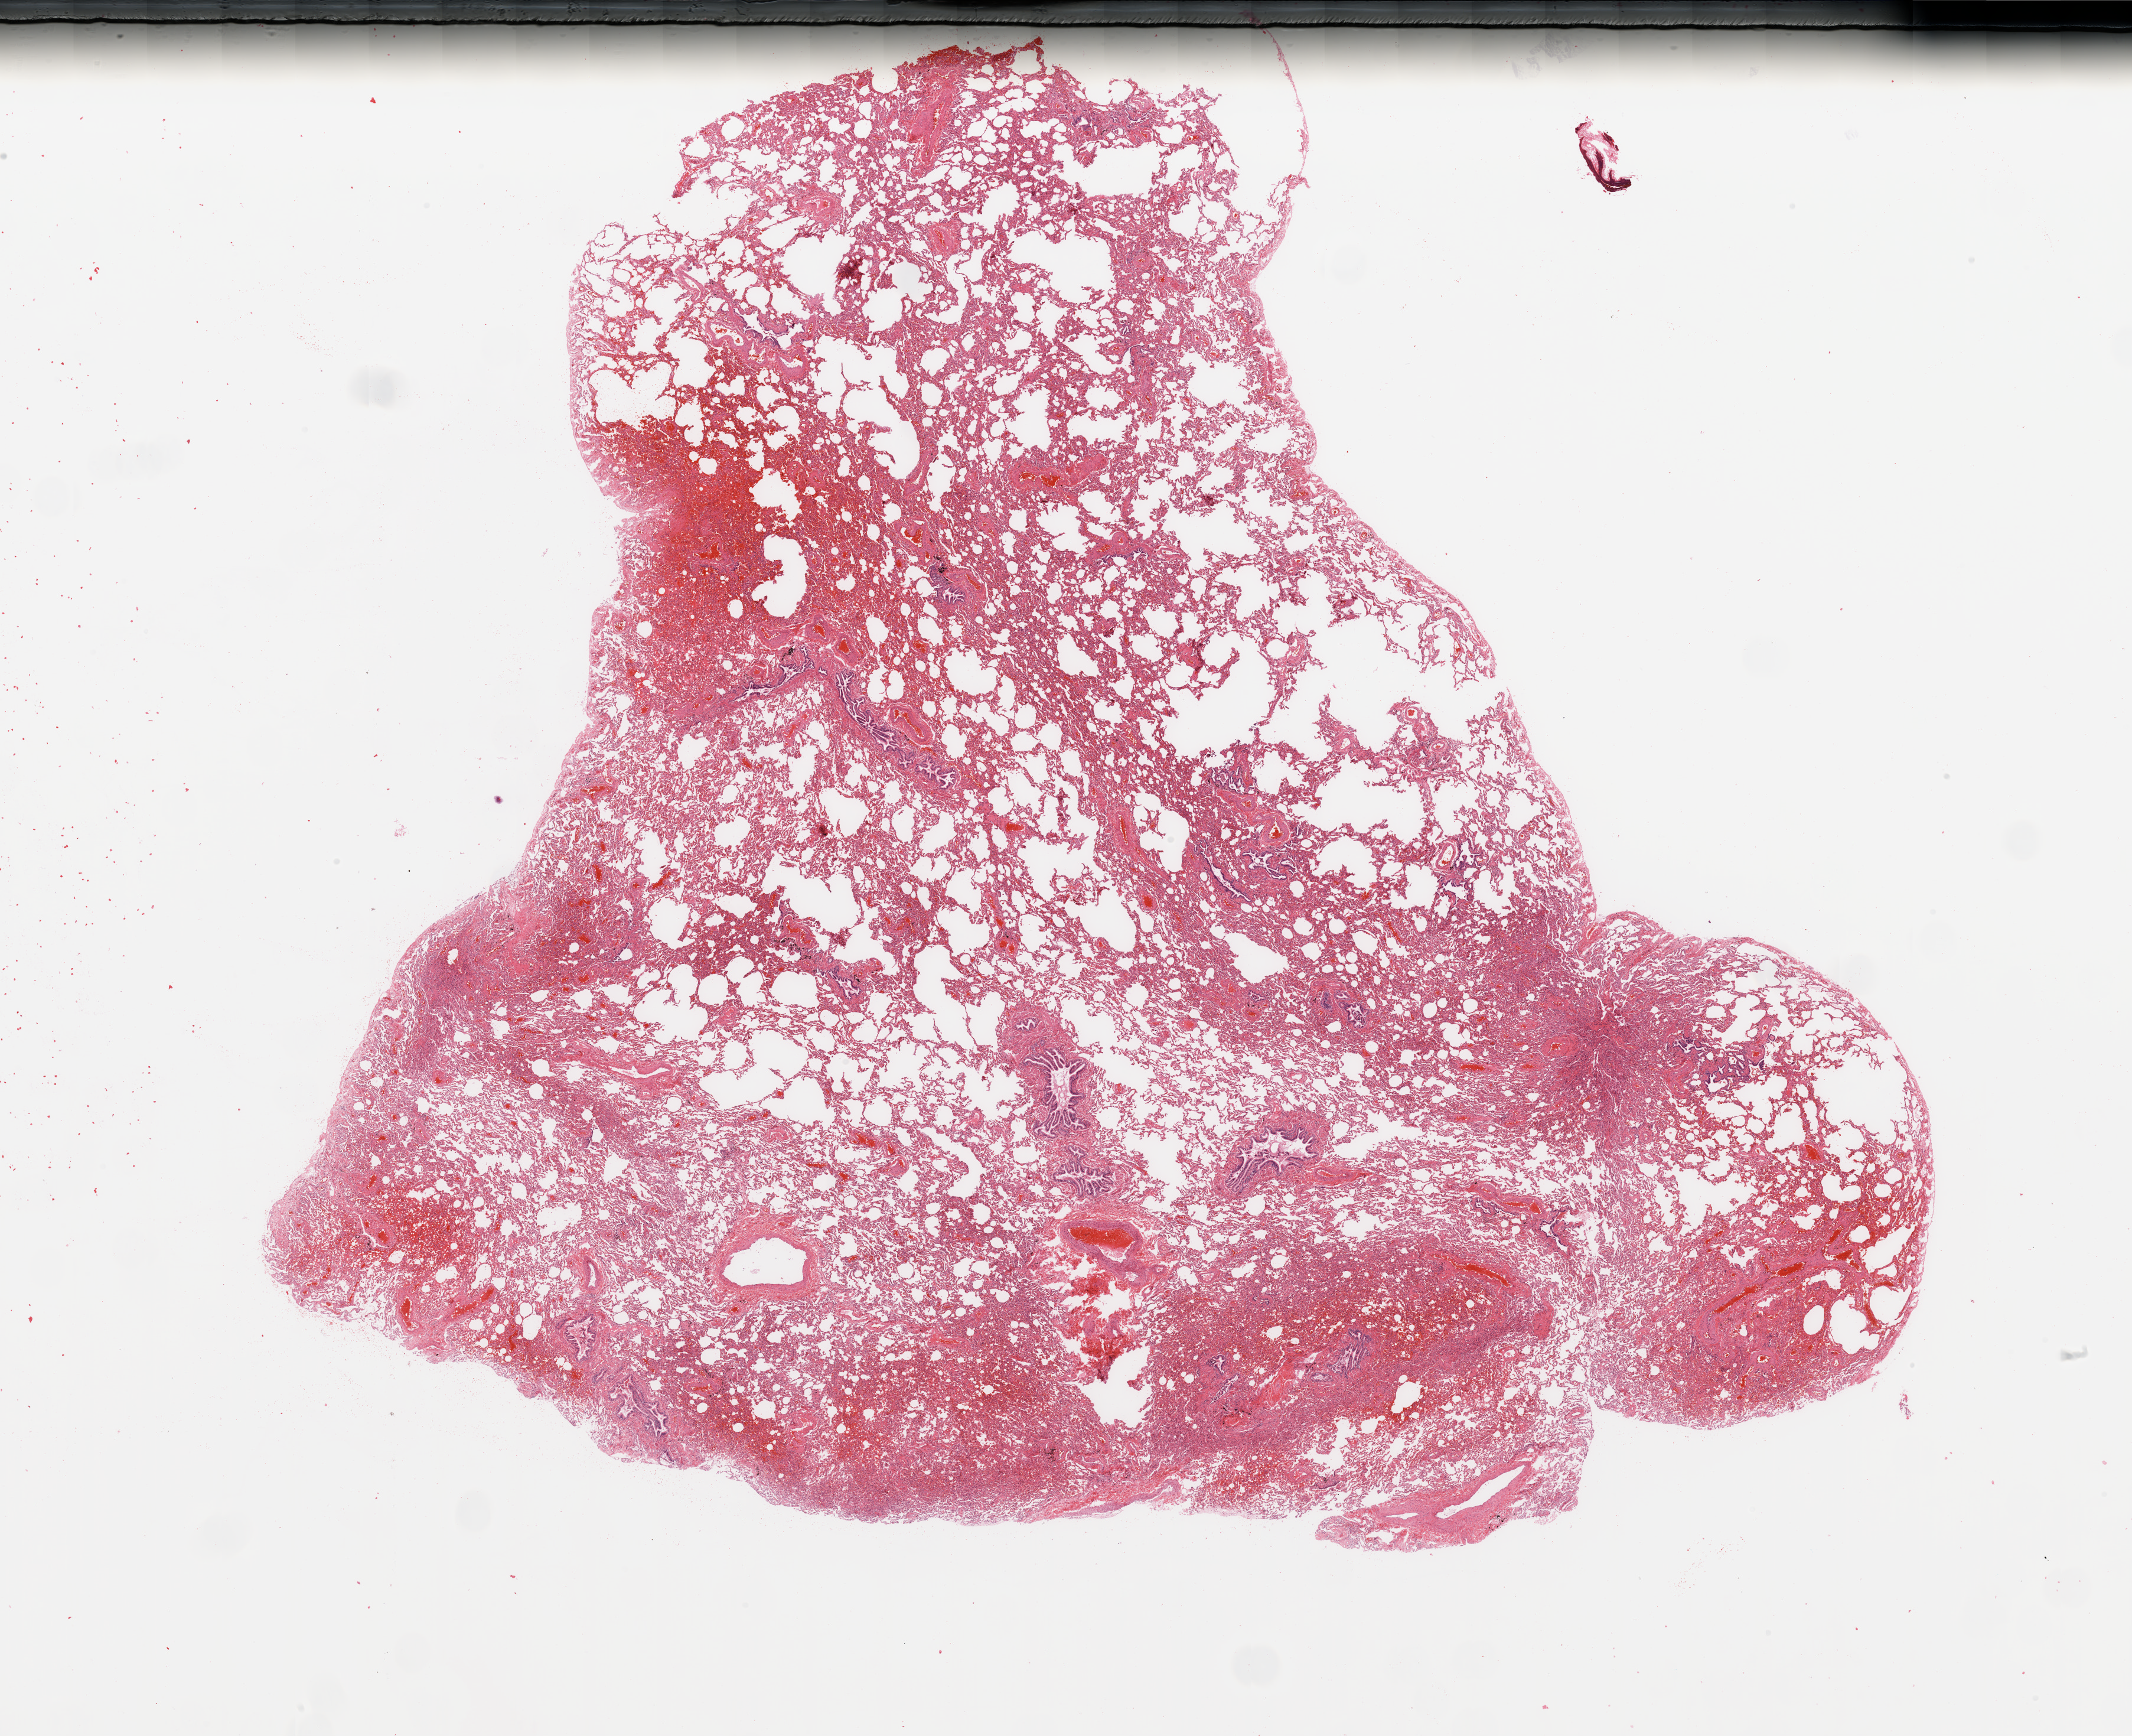
Digitized H&E tissue section (whole slide) — whole scanned area (about 28.5 x 23.2 mm) shown as a low-resolution overview; normal (non-tumour) tissue sample, lung. Patient: female, age 60 years.
This section: normal (non-tumour) tissue from the same patient. Patient diagnosis: Adenocarcinoma, NOS.